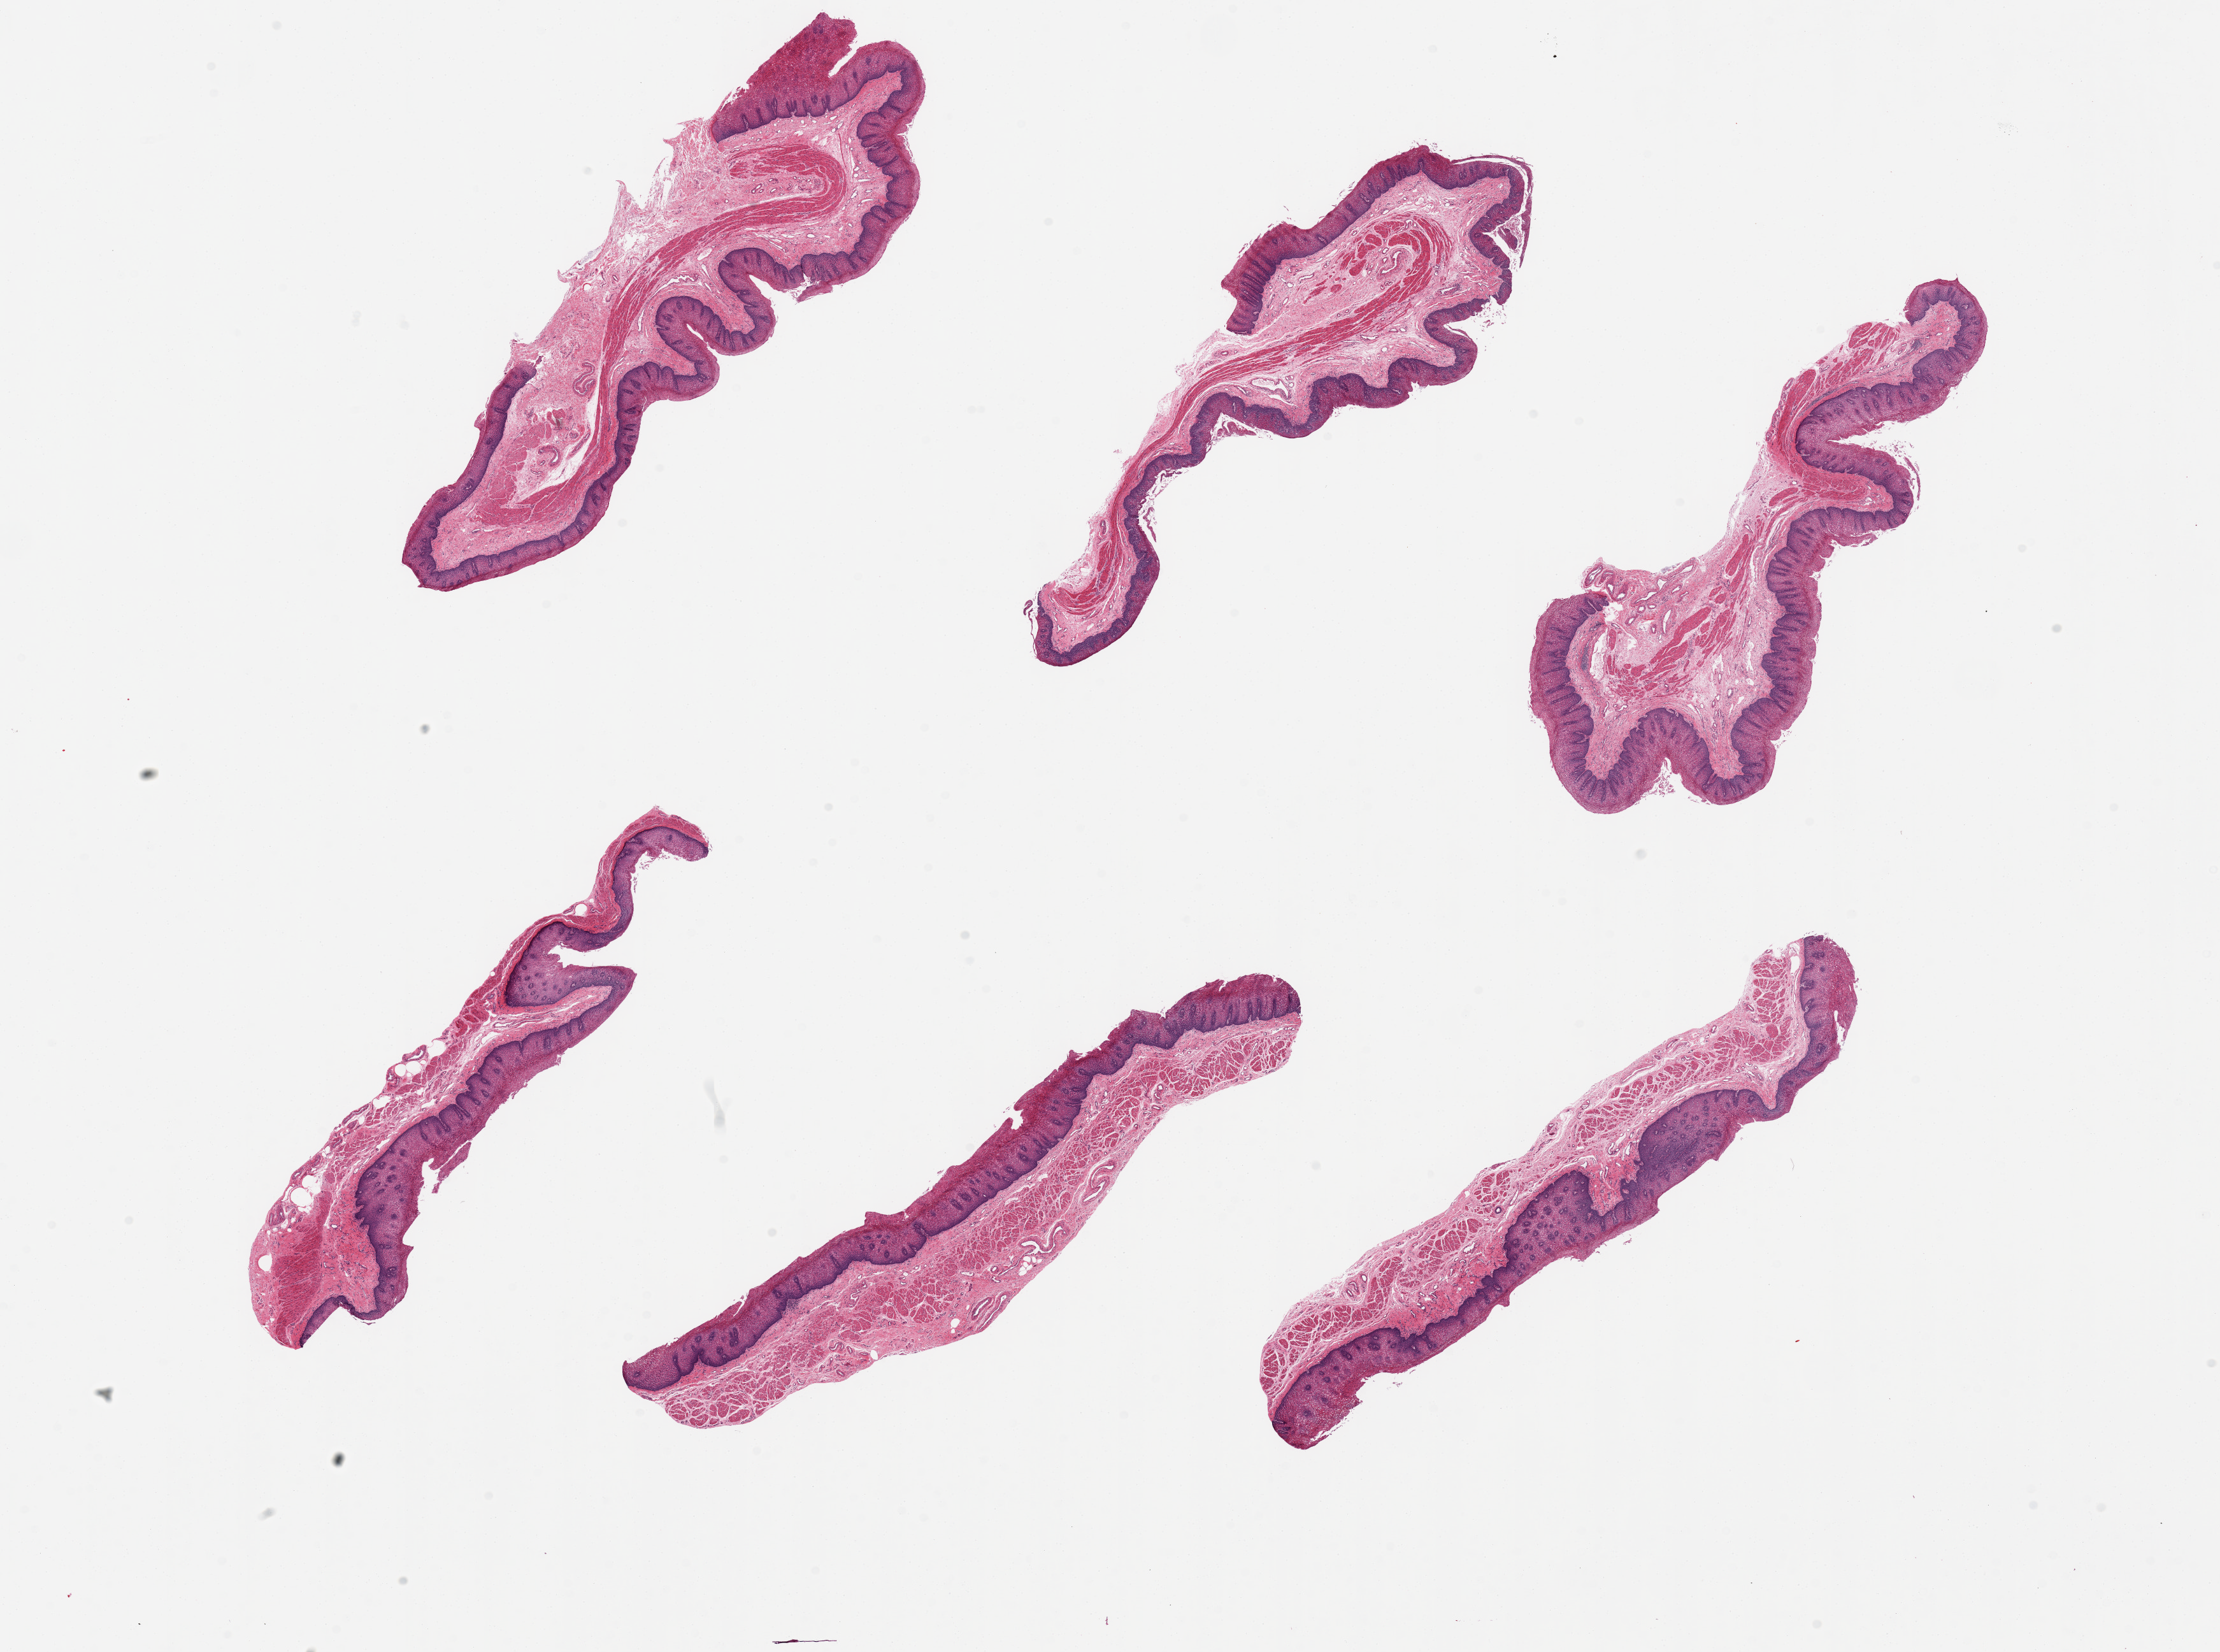
Whole-slide image, haematoxylin and eosin stain, whole scanned area (about 27.6 x 20.5 mm) shown as a low-resolution overview. PAXgene-fixed, paraffin-embedded tissue. Target tissue: esophageal mucous membrane. Donor tissue sample. Female donor.
* review note (as recorded): 6 pieces